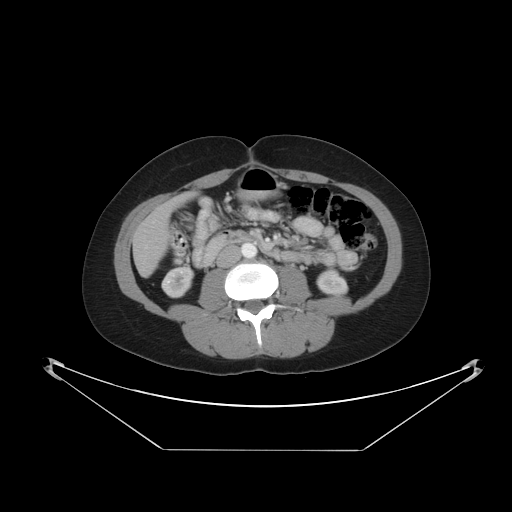
Contrast-enhanced abdominal CT, one axial slice; position 12 of 48 along the scan axis; reconstruction kernel STANDARD; 120 kVp; soft-tissue window (W 400 / L 40 HU); 5 mm slice thickness; 512 × 512 image matrix, field of view 482 × 482 mm. Female patient, age 38 years. From the clinical record (not read from this slice): diagnosis: colorectal cancer liver metastases, imaged before liver resection; multiple liver metastases: yes; largest metastasis: 2.5 cm; disease in both lobes: no.
Annotated regions visible in this slice (expert manual segmentation):
- liver: bounding box [x1, y1, x2, y2] px = [134, 197, 185, 275]
- planned liver remnant (the part of the liver to remain after resection): [180, 197, 183, 203]